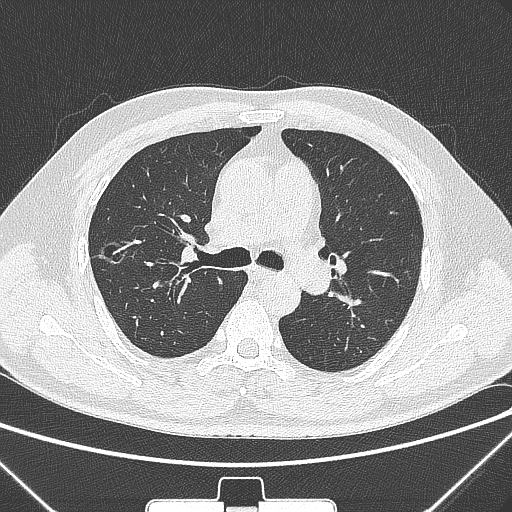
Chest CT, one axial slice. Position 196 of 320 along the scan axis. Lung window (W 1500 / L -600 HU). 512 × 512 image matrix, field of view 350 × 350 mm. Male patient, age 58 years. From the clinical record (not read from this slice): clinical TNM (as recorded): T1c N0 M0; histopathological grade: G2.
Annotated regions visible in this slice (bounding box drawn by a radiologist):
- lung tumour (recorded histology: adenocarcinoma): box from (x=97, y=238) to (x=131, y=274) px